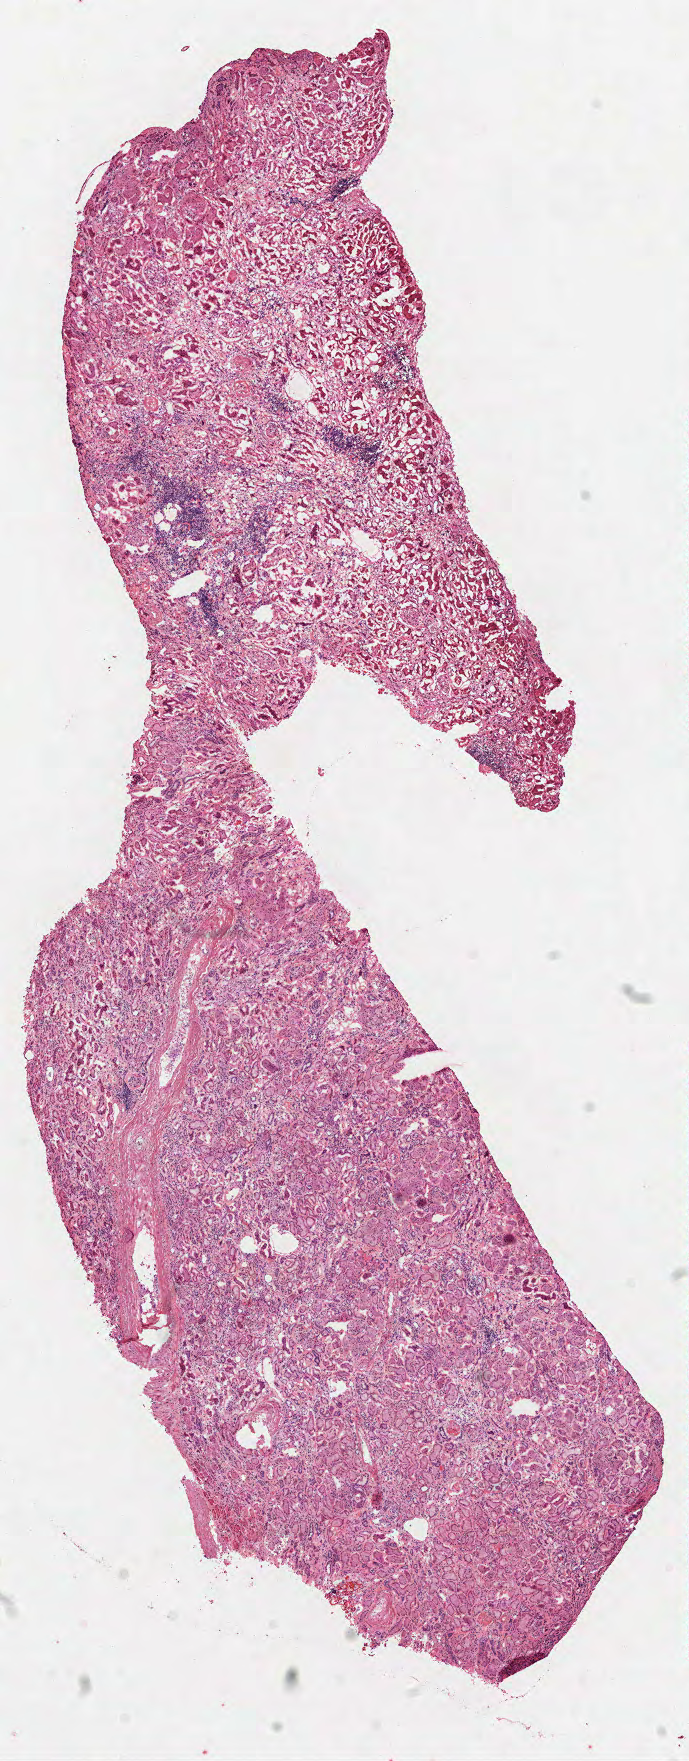
Whole-slide histology image, Hematoxylin and eosin (H&E) stained, low-resolution overview of the scanned area, about 5.6 x 14.2 mm (acquisition: 40x scan); frozen section from the top of the tissue portion; solid tissue normal (non-tumour tissue) sample from the kidney. Male, age 81 years at initial diagnosis.
This section: solid tissue normal (non-tumour) sample from the same patient. Patient diagnosis: Papillary adenocarcinoma, NOS.